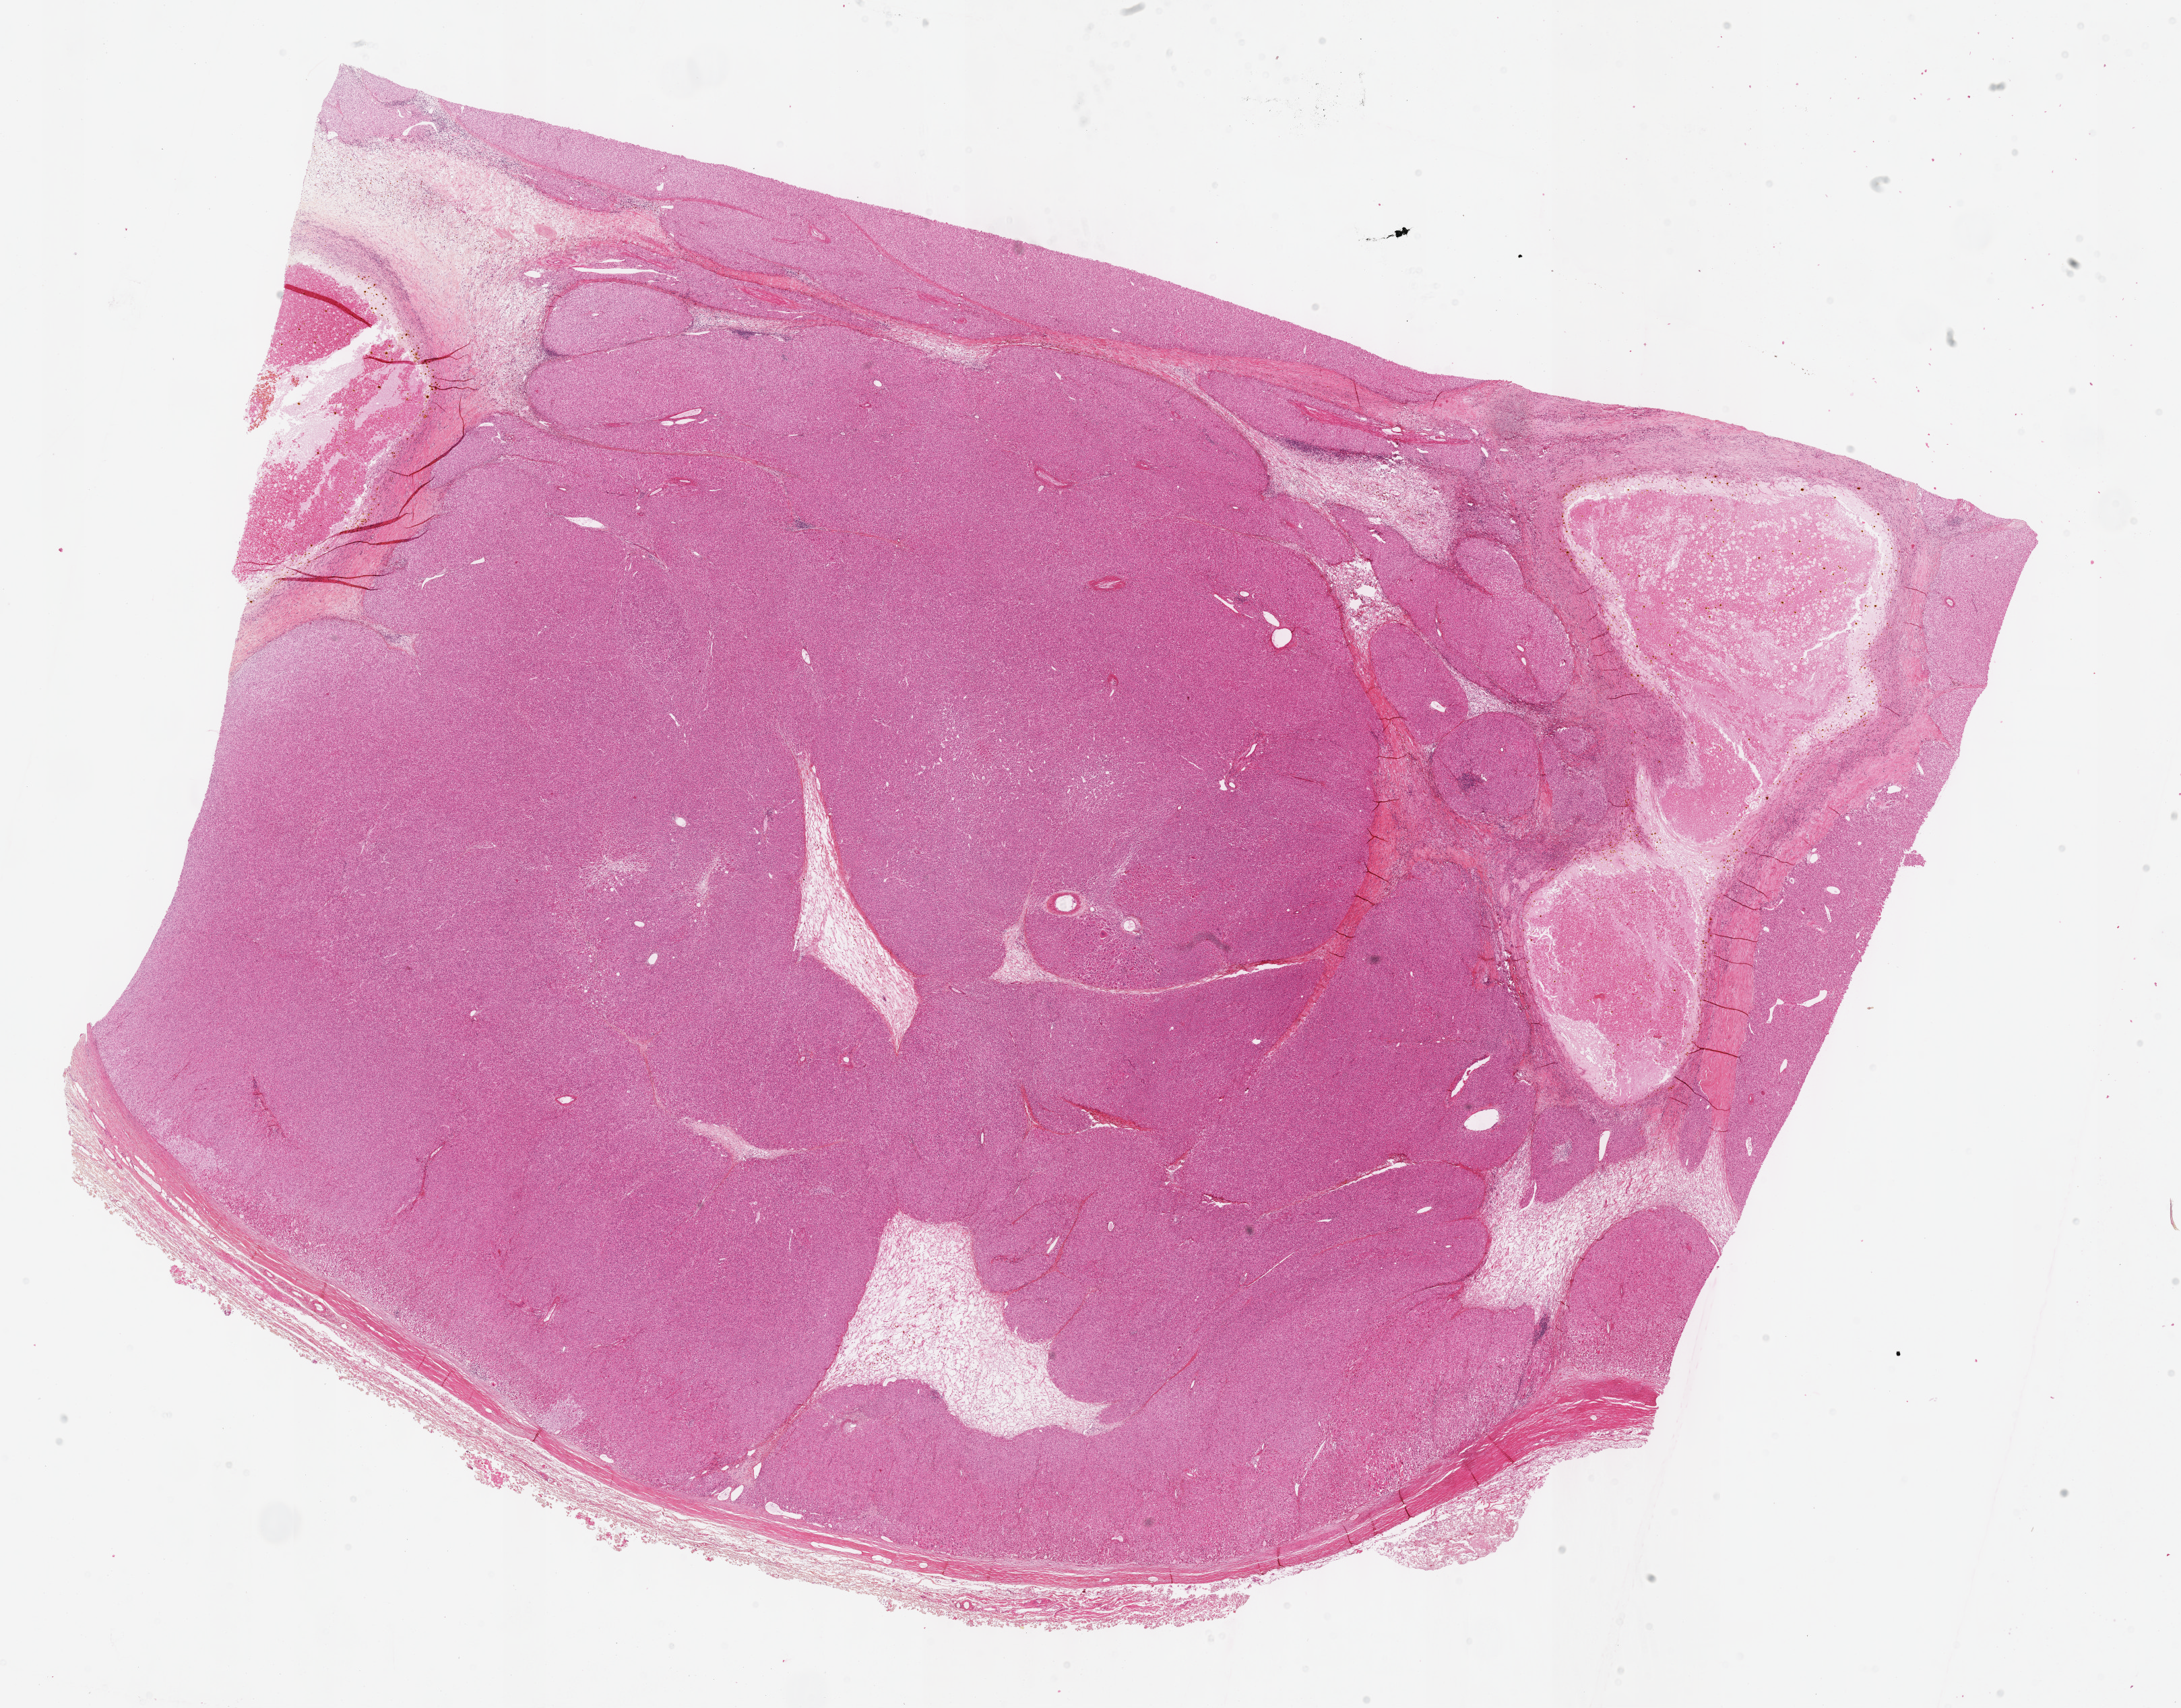
Whole-slide histology image, H&E, a low-resolution overview of the entire scanned area, about 26.2 x 20.5 mm (from a 40x scan); formalin-fixed paraffin-embedded (FFPE) diagnostic section; adrenal cortex, primary tumour sample. Female, age 30 years at initial diagnosis.
• pathologic diagnosis: Adrenal cortical carcinoma